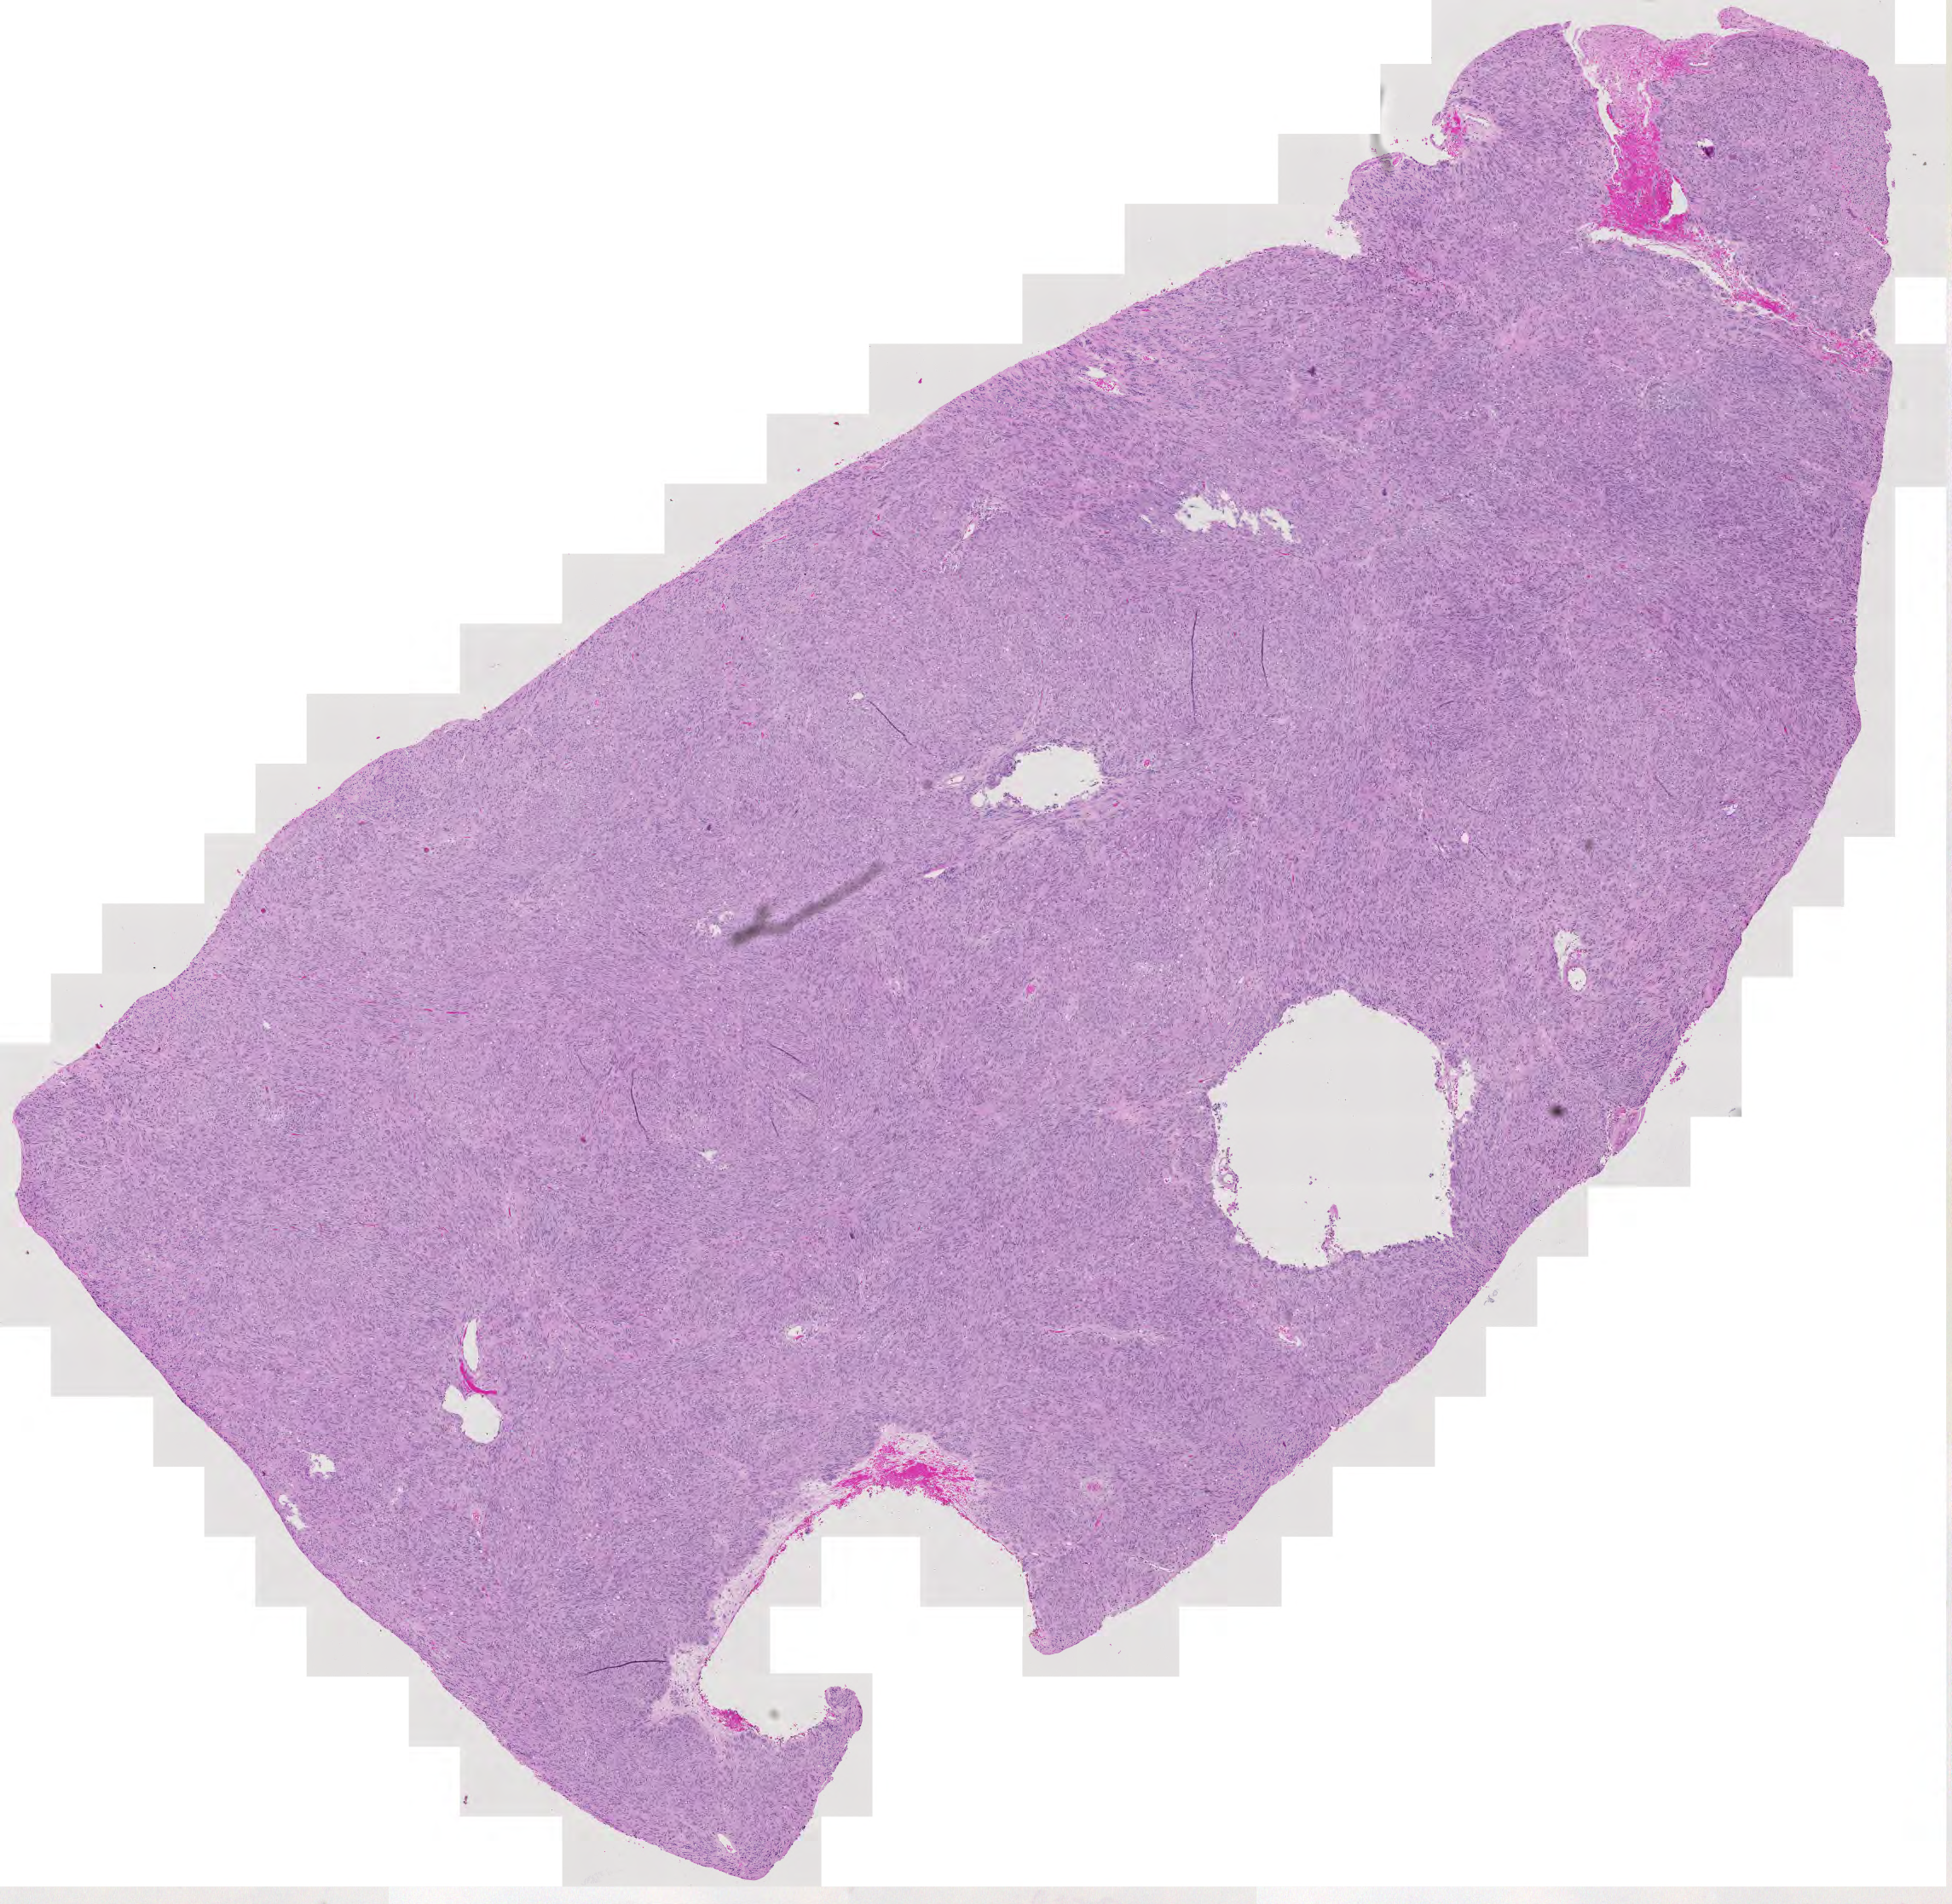
Digitized H&E tissue section (whole slide), shown as a low-resolution overview of the whole scanned area (about 11.8 x 11.5 mm). 87-year-old male patient.
Patient diagnosis (cohort enrolment): sarcoma (site not recorded at cohort level).